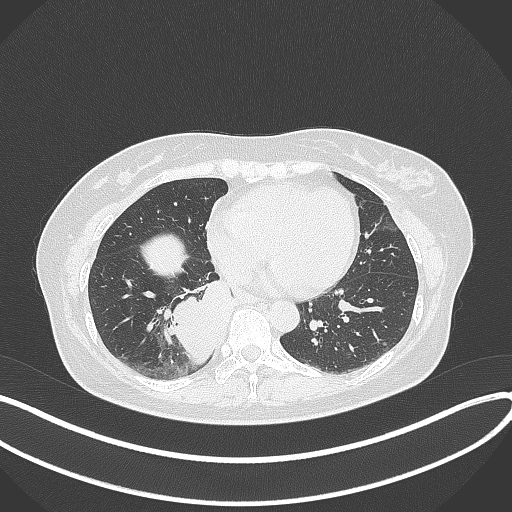
Chest CT, one axial slice. Slice 126 of 331 in the series (ordered by position). Reconstruction kernel B70f. 120 kVp. Lung window (W 1500 / L -600 HU). 512 × 512 image matrix, field of view 400 × 400 mm. Female patient, age 54 years. From the clinical record (not read from this slice): clinical TNM (as recorded): T4 N0 M0.
Annotated regions visible in this slice (bounding box drawn by a radiologist):
- lung tumour (recorded histology: adenocarcinoma): bounding box (x1, y1, x2, y2) in pixels: (170, 277, 237, 371)